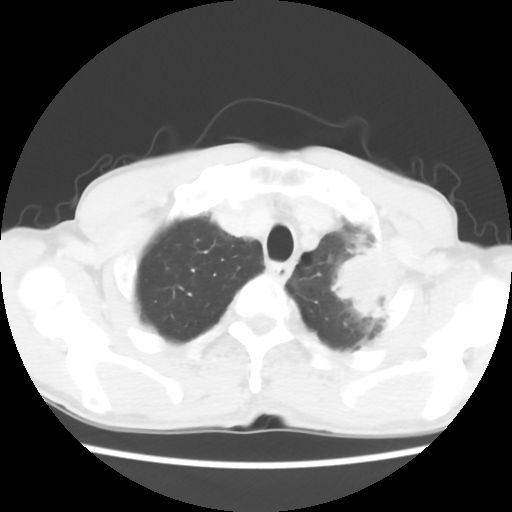
Chest CT, one axial slice. Slice 52 of 60 in the series (ordered by position). Reconstruction kernel STANDARD. 120 kVp. Lung window (W 1500 / L -600 HU). 5 mm slice thickness. 512 × 512 image matrix, field of view 308 × 308 mm. Patient: male, 64 years. From the clinical record (not read from this slice): clinical TNM (as recorded): T3 N3 M0.
Annotated regions visible in this slice (rectangle marked by the reading radiologist):
- lung tumour (recorded histology: adenocarcinoma): box from (x=330, y=243) to (x=407, y=333) px